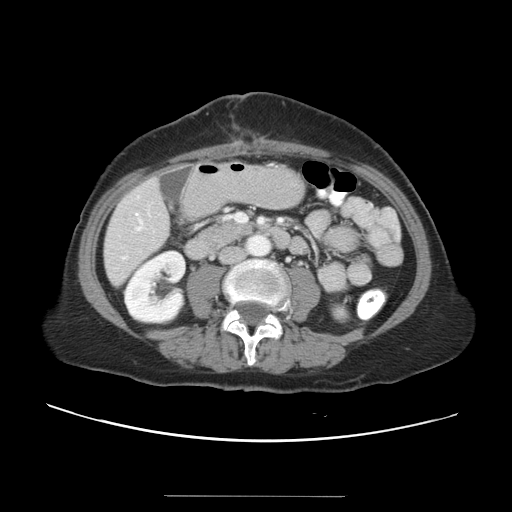
Contrast-enhanced abdominal CT, one axial slice; slice 7 of 34 in the series (ordered by position); reconstruction kernel STANDARD; 120 kVp; intravenous contrast given; soft-tissue window (W 400 / L 40 HU); 5 mm slice thickness; 512 × 512 image matrix, field of view 382 × 382 mm. Female patient, age 69 years. Case-level facts recorded for this patient, not image findings: diagnosis: colorectal cancer liver metastases, imaged before liver resection; multiple liver metastases: yes; largest metastasis: 1.4 cm; disease in both lobes: yes.
Structures marked on this image (expert manual segmentation):
- hepatic veins: bounding box (x1, y1, x2, y2) in pixels: (123, 213, 139, 259)
- liver: (104, 180, 169, 284)
- planned liver remnant (the part of the liver to remain after resection): (104, 232, 165, 284)
- portal vein (with intrahepatic branches): (137, 213, 281, 230)